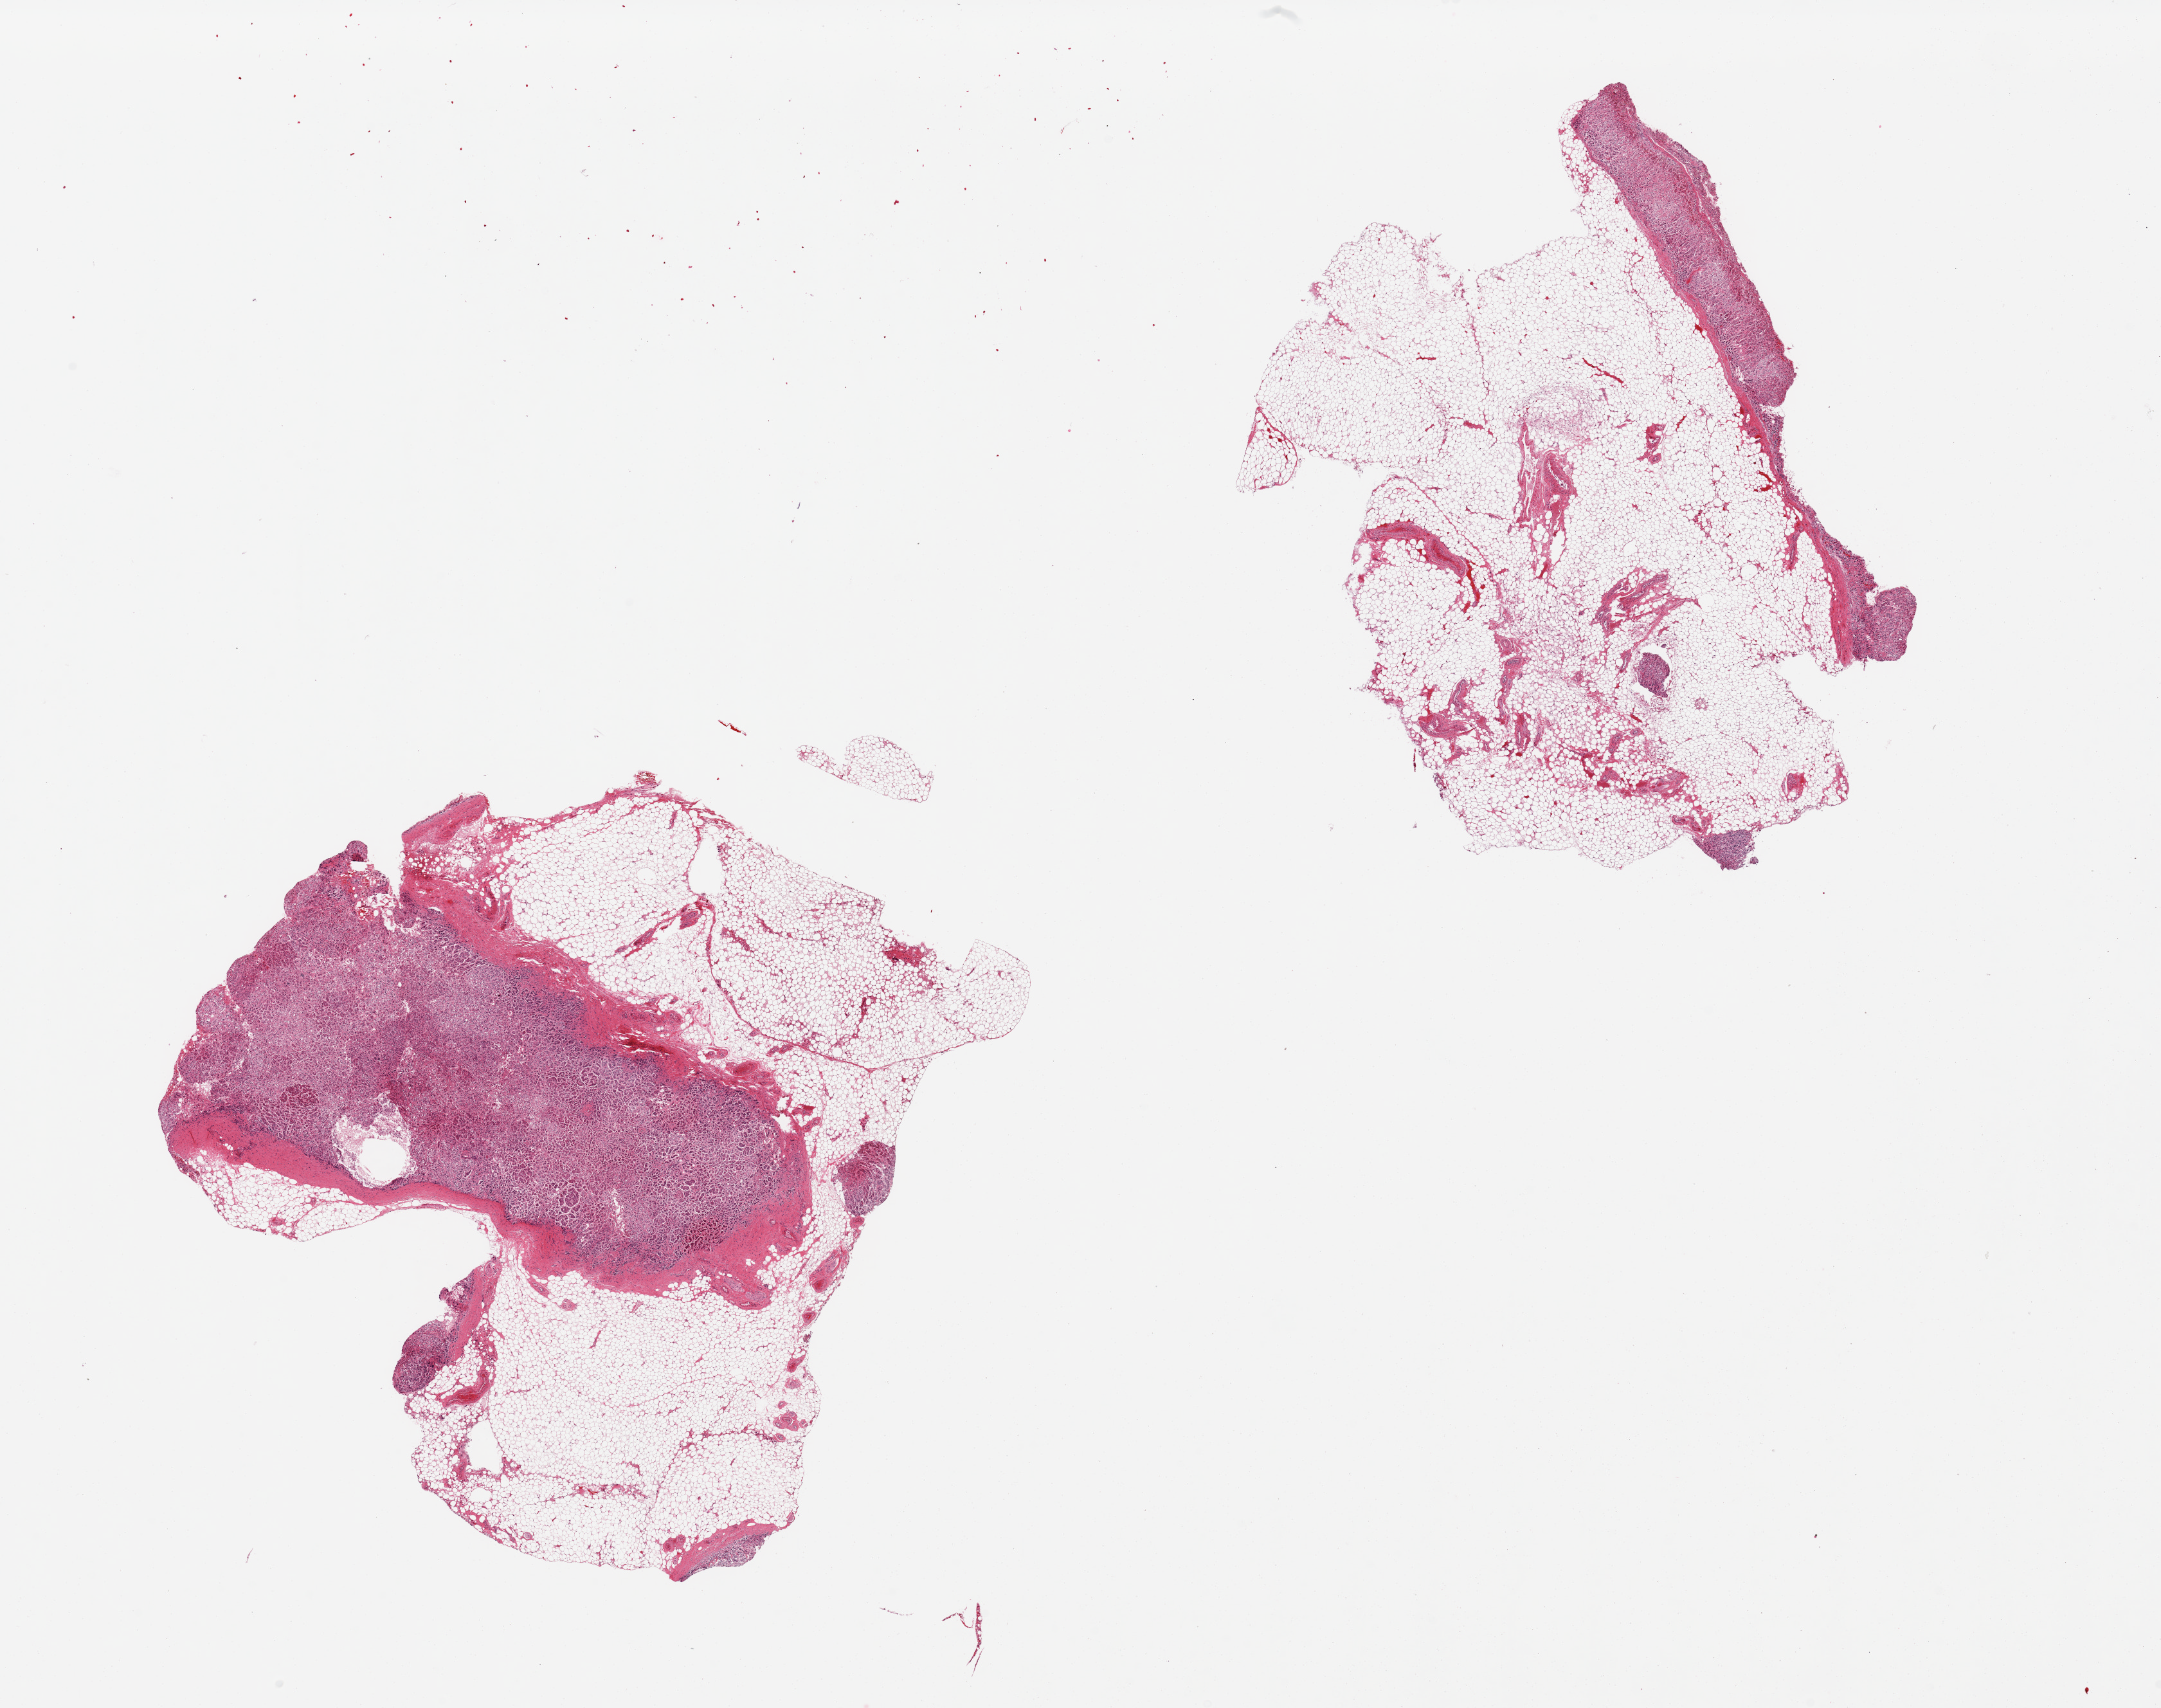
Whole-slide image, H&E stain — low-resolution overview of the scanned area, about 26.6 x 21.0 mm, PAXgene-fixed, paraffin-embedded tissue, target tissue: adrenal gland, donor tissue sample.
Review note (as recorded): 2 pieces; 1 is 50% fat, the other is 90% fat.